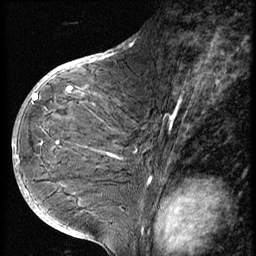
Breast MRI (dynamic contrast-enhanced), one sagittal slice. Slice 33 of 56 in the series (ordered by position). 3 images stored at this slice position (order not interpretable as contrast timing). 1.5 T. TE 4.2 ms, TR 9 ms. 2.5 mm slice thickness. 256 × 256 image matrix. Female patient, age 49 years. From the clinical record (not read from this slice): setting: breast cancer imaged before/during neoadjuvant chemotherapy; receptor status: HER2-positive.
Structures marked on this image (semi-automatically segmented with operator editing):
- analysis volume of interest (the breast-tissue region the enhancement analysis was run in; not a lesion): bounding box (x1, y1, x2, y2) in pixels: (37, 85, 131, 207)
- tumour enhancement mask (voxels above the 140 % enhancement threshold inside the analysis volume of interest): (37, 87, 72, 100)